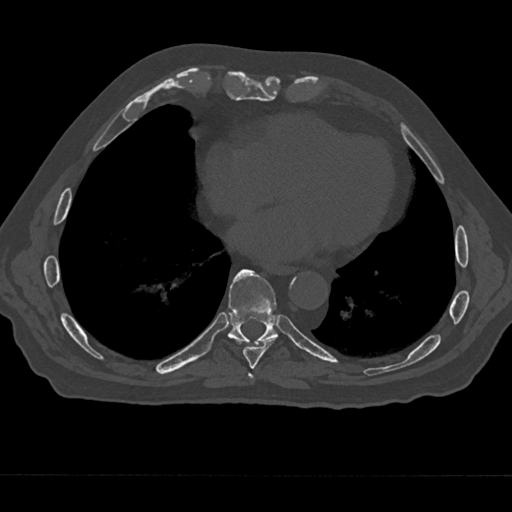
CT including the spine, one axial slice; position 289 of 797 along the scan axis; reconstruction kernel Br40s/3; 120 kVp; bone window (W 1800 / L 400 HU); 512 × 512 image matrix. Male patient, age 75 years. From the clinical record (not read from this slice): primary cancer: renal; vertebrae with lytic lesions (as recorded): T4.
Annotated regions visible in this slice (semi-automatic segmentation, software-assisted and operator-edited):
- T7 vertebra: bounding box <248,373,255,383> (left, top, right, bottom; pixels)
- T8 vertebra: <235,337,277,369>
- T9 vertebra: <228,269,278,344>